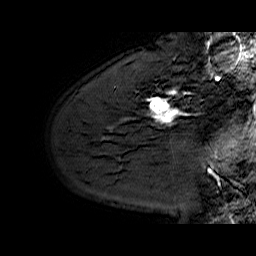
Breast MRI (dynamic contrast-enhanced), one sagittal slice; slice 47 of 60 in the series (ordered by position); dynamic contrast-enhanced series, time point 2 of 6 at this slice position (early post-contrast); 1.5 T; TE 6.4 ms, TR 32.9 ms; 256 × 256 image matrix, field of view 200 × 200 mm. Female patient. From the clinical record (not read from this slice): setting: breast cancer imaged before/during neoadjuvant chemotherapy; receptor status: HER2-positive.
Annotated regions visible in this slice (semi-automatic segmentation, software-assisted and operator-edited):
- analysis volume of interest (the breast-tissue region the enhancement analysis was run in; not a lesion): box from (x=130, y=62) to (x=210, y=128) px
- tumour enhancement mask (voxels above the 100 % enhancement threshold inside the analysis volume of interest): (x=149, y=88)–(x=175, y=125)